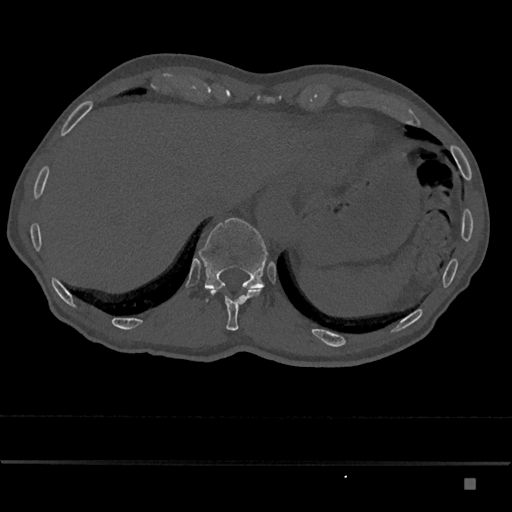
CT including the spine, one axial slice; position 644 of 797 along the scan axis; reconstruction kernel Br40s/3; 120 kVp; bone window (W 1800 / L 400 HU); 512 × 512 image matrix. Male patient, age 72 years. From the clinical record (not read from this slice): primary cancer: prostate.
Outlined on this slice (semi-automatic segmentation, software-assisted and operator-edited):
- T11 vertebra: bounding box (x1, y1, x2, y2) in pixels: (210, 288, 262, 331)
- T12 vertebra: (199, 218, 268, 303)